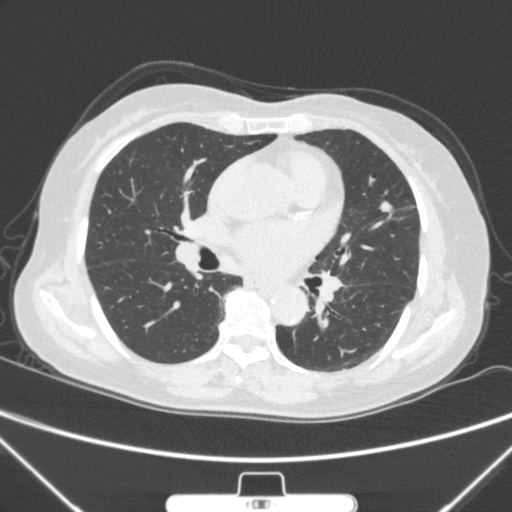
Chest CT, one axial slice. Slice 146 of 300 in the series (ordered by position). Lung window (W 1500 / L -600 HU). 512 × 512 image matrix, field of view 350 × 350 mm. Female patient, age 70 years. From the clinical record (not read from this slice): clinical TNM (as recorded): T1b N0 M0; histopathological grade: G2.
Annotated regions visible in this slice (bounding box drawn by a radiologist):
- lung tumour (recorded histology: adenocarcinoma): bounding box <369,192,407,228> (left, top, right, bottom; pixels)